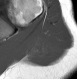
MRI of an extremity soft-tissue mass, one axial slice; position 17 of 28 along the scan axis; MR volume resampled by the dataset authors to the PET/CT grid (not the native acquisition matrix); 3.27 mm slice thickness; 77 × 79 image matrix, field of view 75 × 77 mm. Female patient. Case-level facts recorded for this patient, not image findings: histological type: malignant fibrous histiocytoma; grade: low; site of the primary tumour: left arm.
Annotated regions visible in this slice (expert contour drawn on MRI and transferred to this co-registered scan by the dataset authors):
- gross tumour volume (mass): bounding box [x1, y1, x2, y2] px = [28, 34, 52, 60]